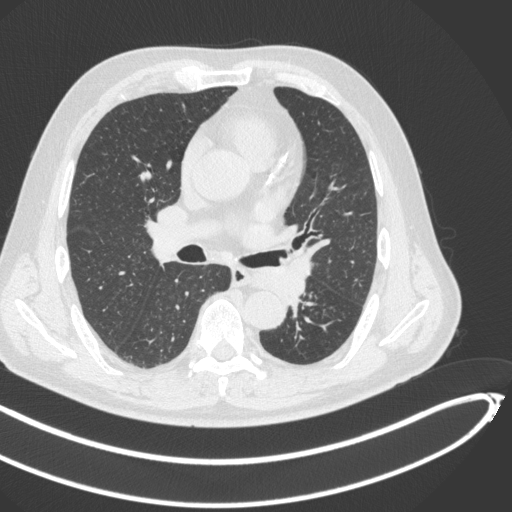
Chest CT, one axial slice. 120 kVp. Lung window (W 1500 / L -600 HU). 1 mm slice thickness. 512 × 512 image matrix, field of view 400 × 400 mm. Male patient, age 64 years. From the clinical record (not read from this slice): clinical TNM (as recorded): T1c N0 M0.
Outlined on this slice (rectangle marked by the reading radiologist):
- lung tumour (recorded histology: squamous cell carcinoma): bounding box (x1, y1, x2, y2) in pixels: (248, 255, 315, 305)